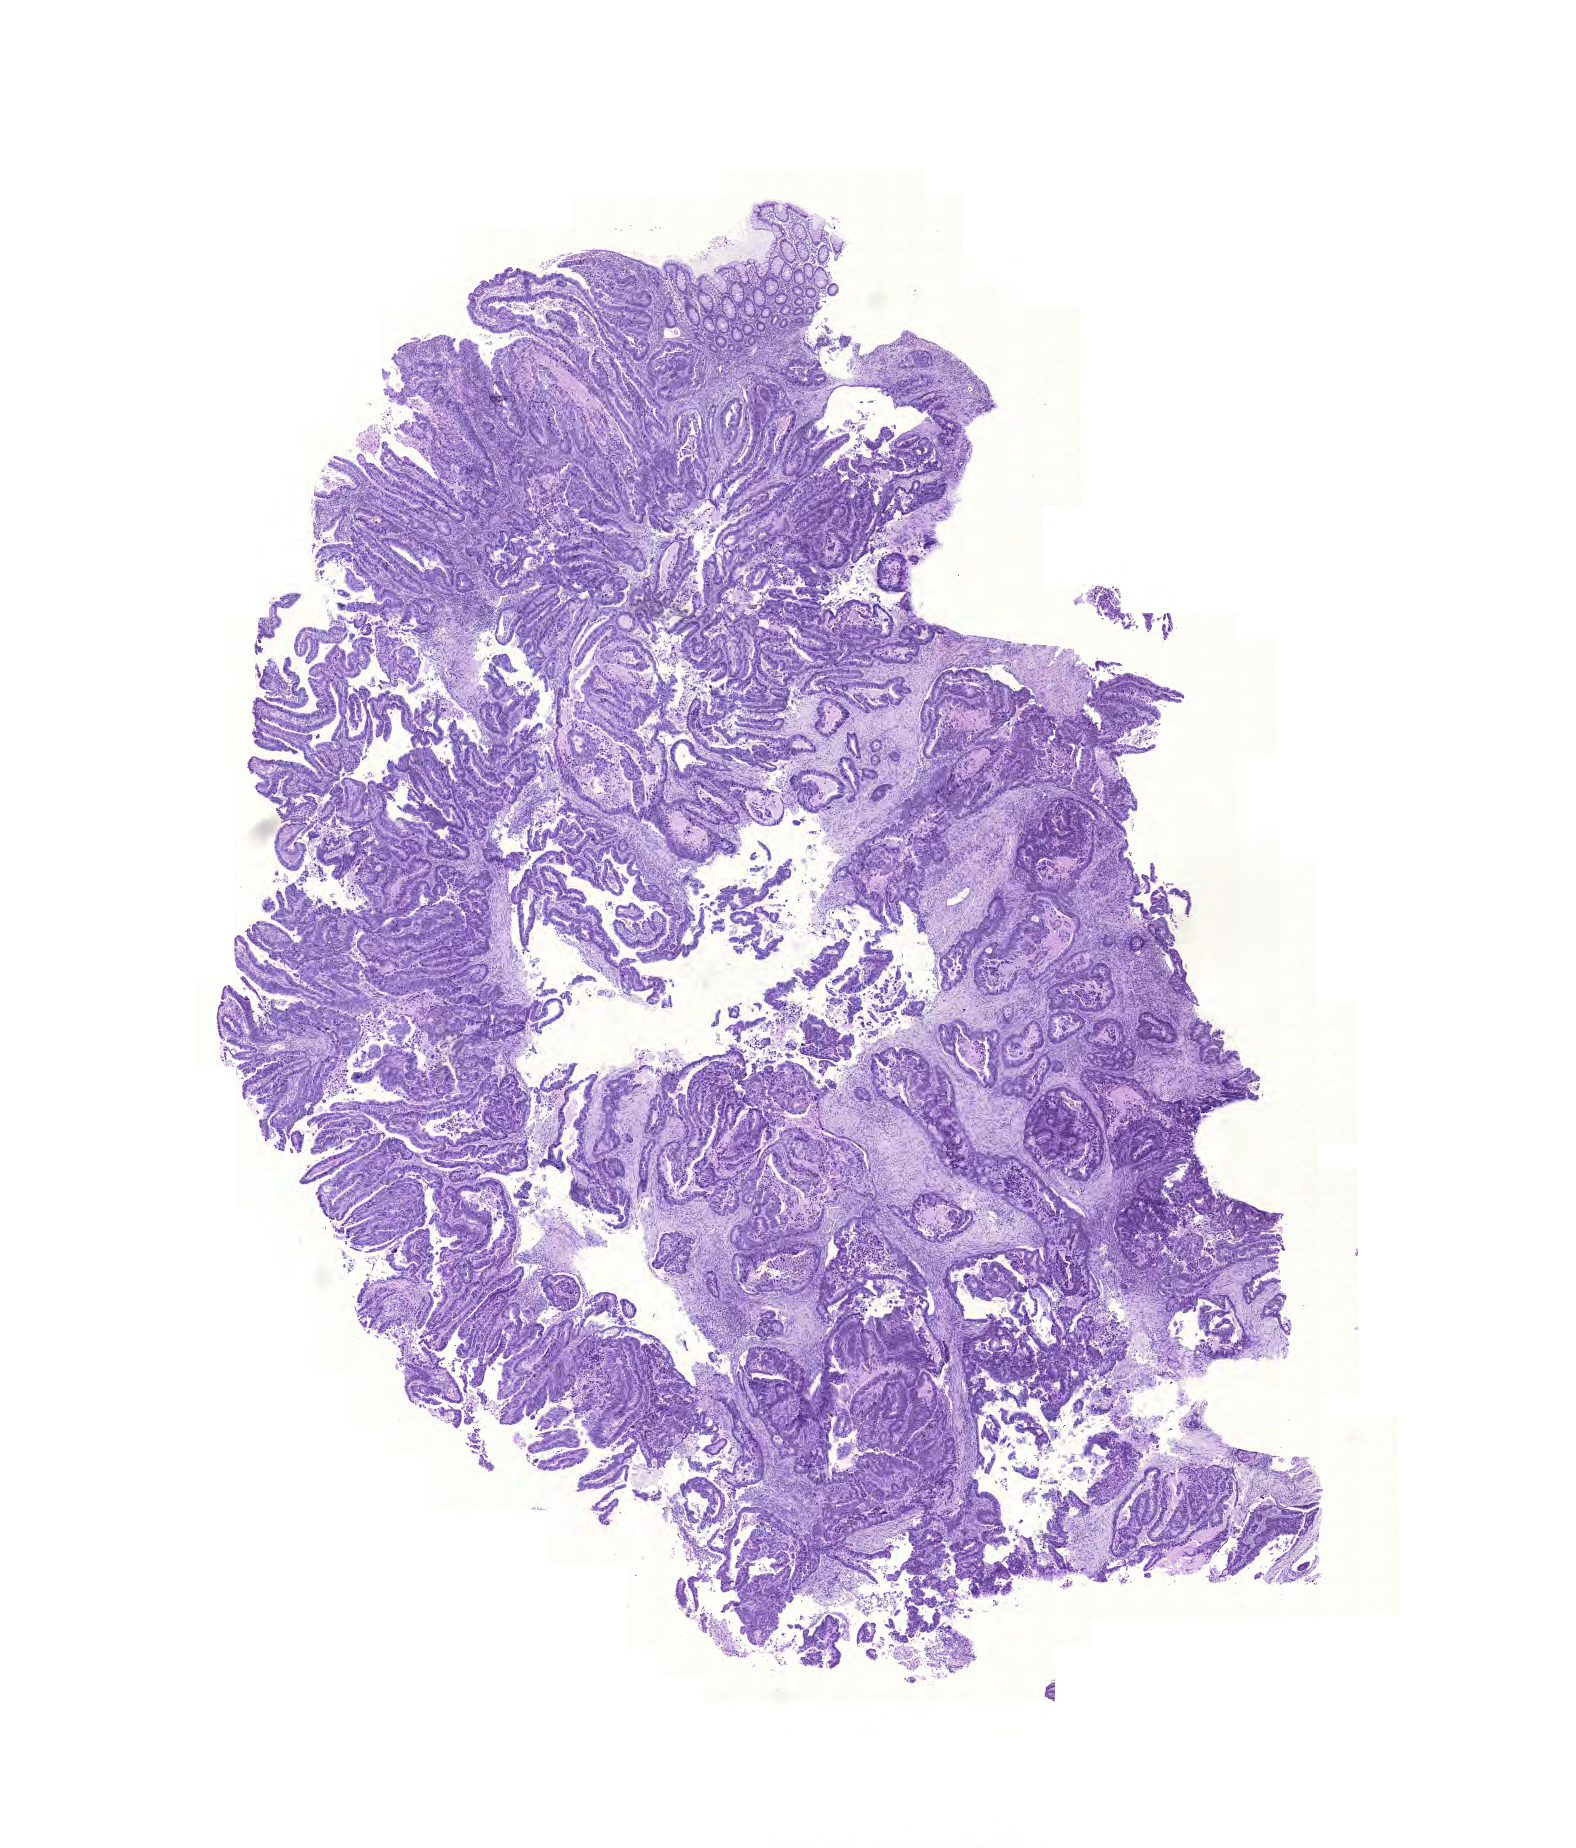
Digitized H&E-stained tissue section (whole slide), a low-resolution overview of the entire scanned area, about 11.7 x 13.7 mm (from a 20x scan), formalin-fixed paraffin-embedded (FFPE) diagnostic section, colon, primary tumour sample. Patient: male, age at initial diagnosis 60 years.
* lymph nodes positive (case pathology): 0 of 54 examined
* AJCC pathologic stage: IIA (6th edition)
* TNM: T3 N0 M0
* pathologic diagnosis: Adenocarcinoma, NOS